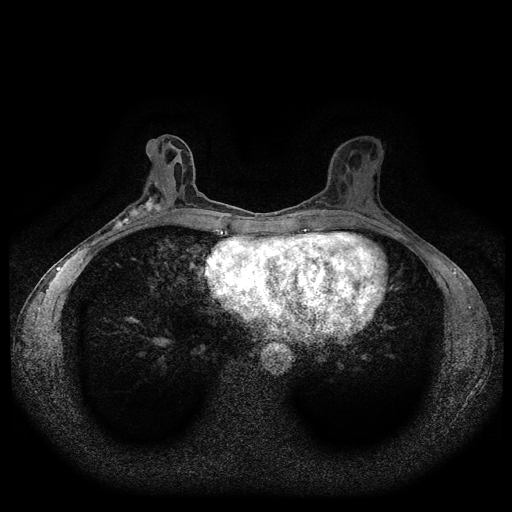
Breast MRI (dynamic contrast-enhanced, multi-phase), one axial slice. Slice 45 of 116 in the series (ordered by position). Dynamic contrast-enhanced series, time point 2 of 5 at this slice position (early post-contrast). 1.5 T. TE 2.6 ms, TR 5.3 ms. 2 mm slice thickness. 512 × 512 image matrix. Patient: female, 50 years.
Annotated regions visible in this slice (semi-automatically segmented with operator editing):
- breast lesion (labelled 'tumour' in the annotation; benign lesions carry a separate 'benign' label): bounding box (x1, y1, x2, y2) in pixels: (110, 193, 164, 231)